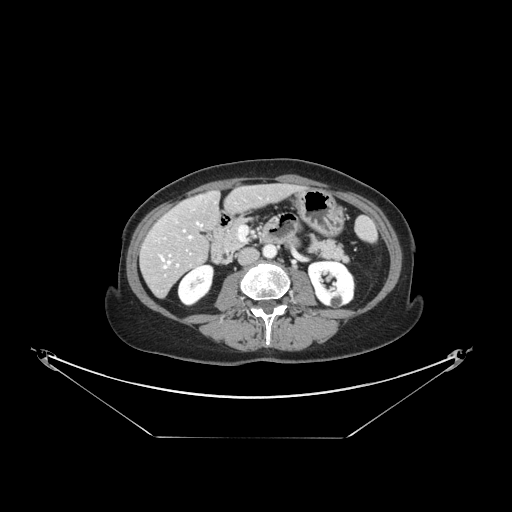
Contrast-enhanced abdominal CT, one axial slice; position 52 of 148 along the scan axis; reconstruction kernel STANDARD; 120 kVp; intravenous contrast given; soft-tissue window (W 400 / L 40 HU); 2.5 mm slice thickness; 512 × 512 image matrix, field of view 500 × 500 mm. Female patient, age 73 years. Case-level facts recorded for this patient, not image findings: diagnosis: colorectal cancer liver metastases, imaged before liver resection; multiple liver metastases: no; largest metastasis: 1 cm; disease in both lobes: no.
Structures marked on this image (expert manual segmentation):
- hepatic veins: bounding box [x1, y1, x2, y2] px = [161, 222, 202, 268]
- liver: [143, 184, 294, 296]
- planned liver remnant (the part of the liver to remain after resection): [162, 185, 294, 248]